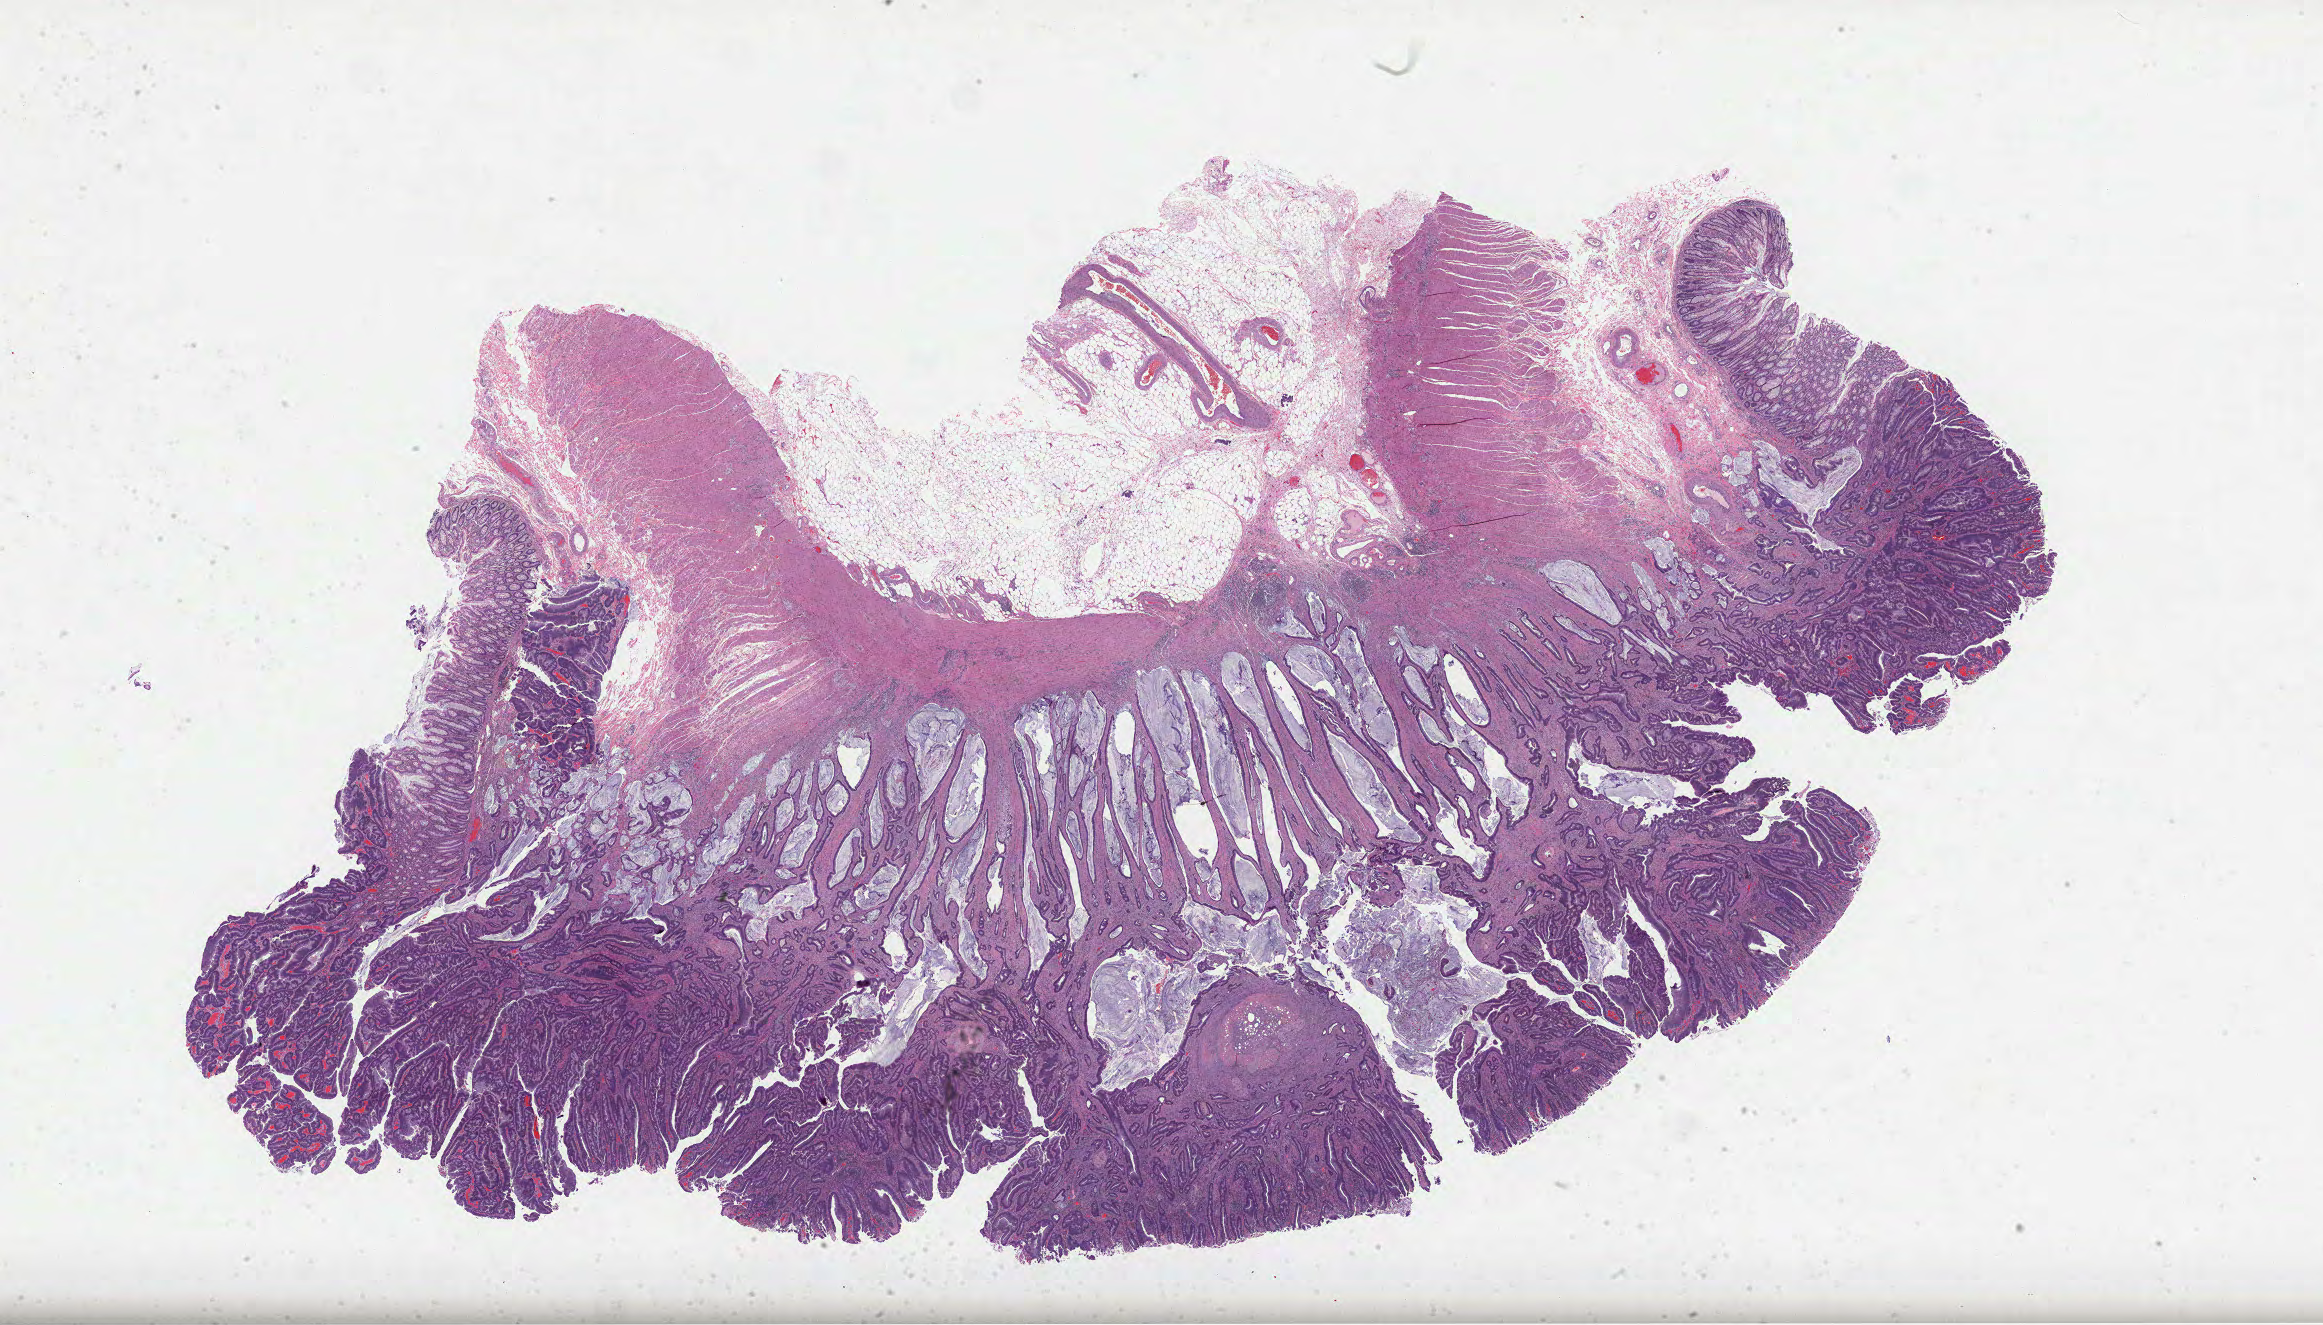
Digitized H&E tissue section (whole slide), a low-resolution overview of the entire scanned area, about 37.5 x 21.4 mm (acquisition: 40x scan). Formalin-fixed paraffin-embedded (FFPE) diagnostic section. Primary tumour sample from the colon. Female, age 78 years at initial diagnosis.
Histologic diagnosis: Adenocarcinoma, NOS (cecum). AJCC pathologic stage: IIIB. TNM: T3 N2a M0. Lymph nodes positive (case pathology): 4 of 17 examined.